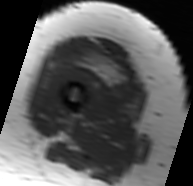
MRI of an extremity soft-tissue mass, one axial slice; position 21 of 91 along the scan axis; MR volume resampled by the dataset authors to the PET/CT grid (not the native acquisition matrix); 3.27 mm slice thickness; 193 × 186 image matrix, field of view 188 × 182 mm. Female patient. From the clinical record (not read from this slice): histological type: malignant solitary fibrous tumor; grade: intermediate; site of the primary tumour: right thigh.
Structures marked on this image (expert contour drawn on MRI and transferred to this co-registered scan by the dataset authors):
- gross tumour volume including surrounding oedema: box from (x=63, y=37) to (x=139, y=86) px